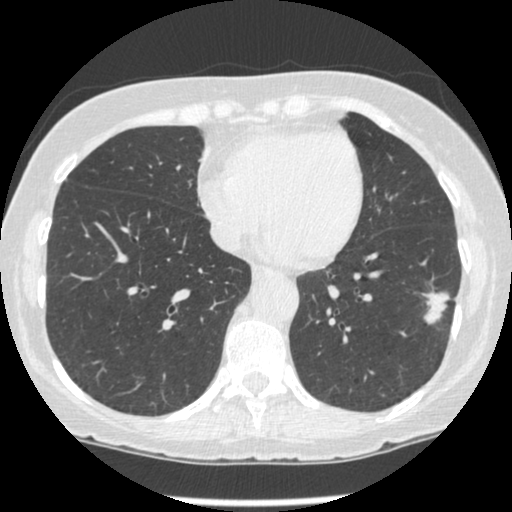
Low-dose screening chest CT, one axial slice. Position 88 of 247 along the scan axis. Reconstruction kernel STANDARD. 120 kVp. Lung window (W 1500 / L -600 HU). 512 × 512 image matrix.
Annotated regions visible in this slice (outlined manually by an expert reader):
- lesion 1 (tumor, lower lobe of left lung): bounding box [x1, y1, x2, y2] px = [423, 291, 450, 324]